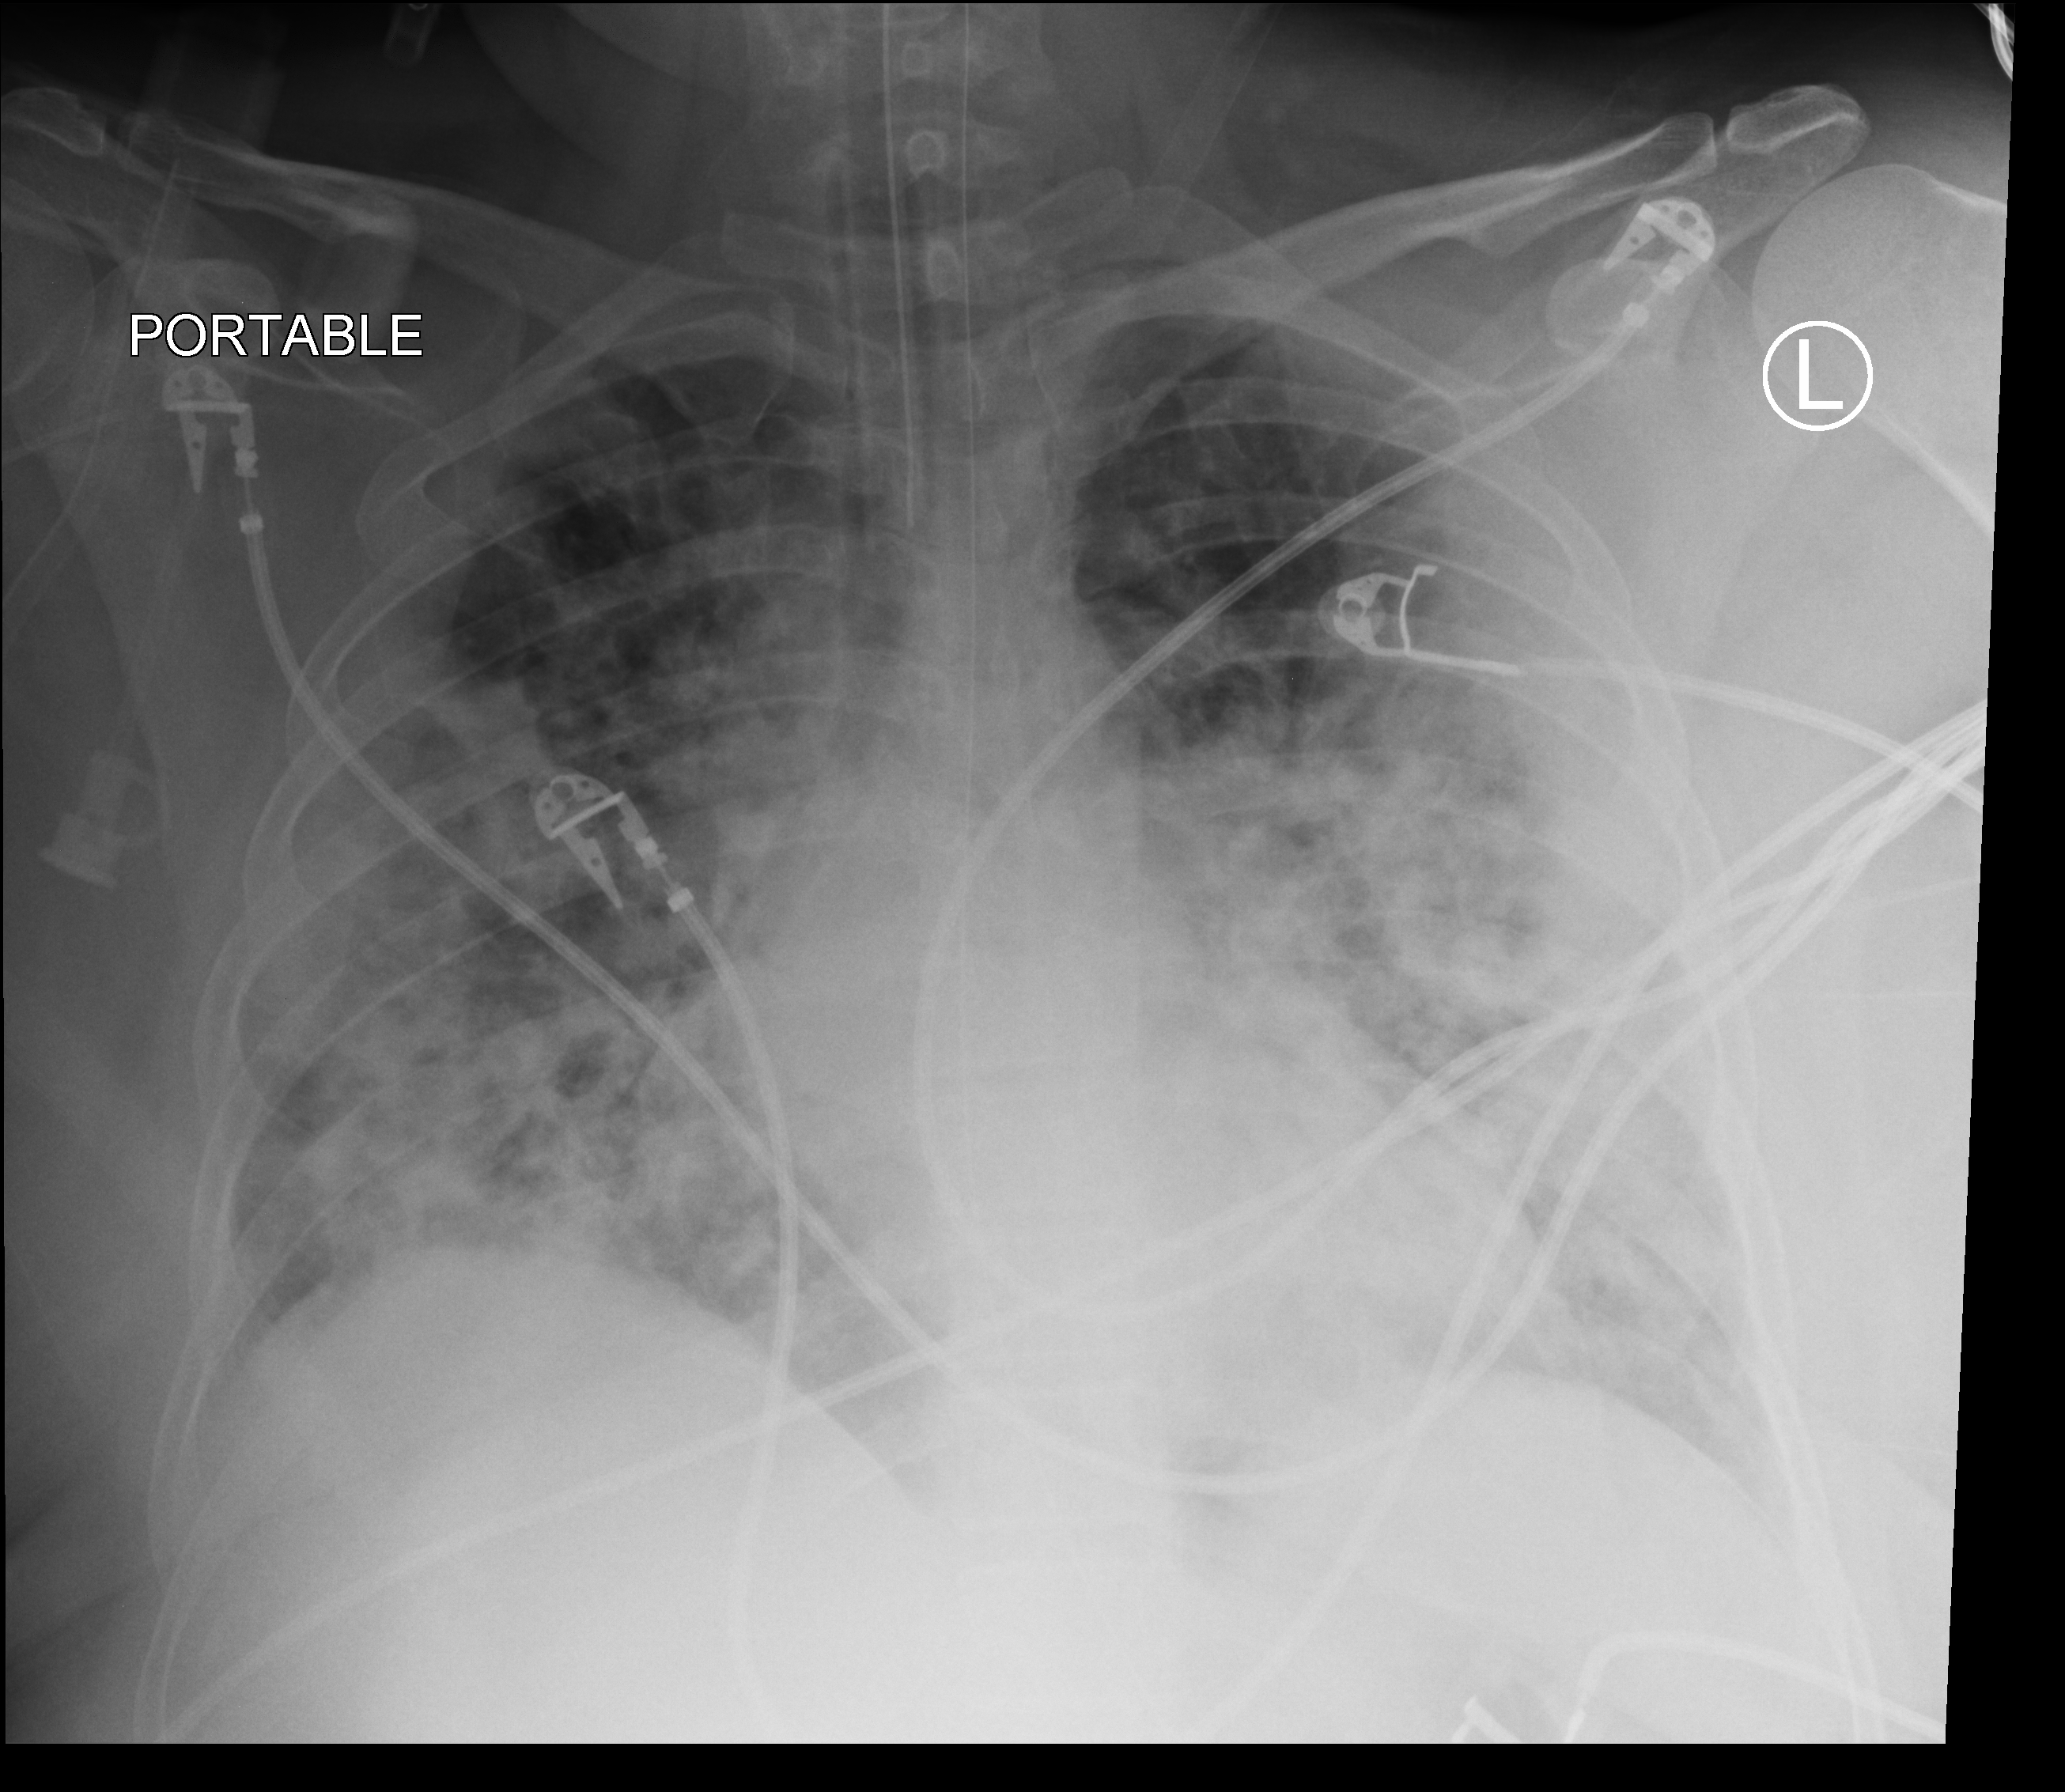
Portable chest radiograph; anteroposterior (AP) projection. Female patient hospitalised with COVID-19, age 18–59 years.
From the hospital-stay record, not from the radiograph (when in the stay this image was taken is not recorded):
- diabetes (admission record): yes